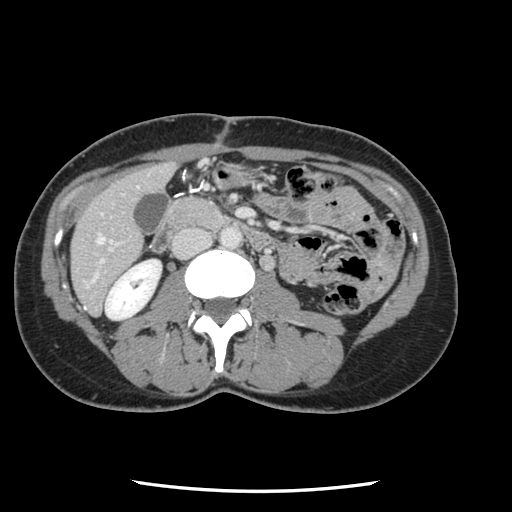
Contrast-enhanced abdominal CT, one axial slice; slice 28 of 134 in the series (ordered by position); intravenous contrast given; soft-tissue window (W 400 / L 40 HU); 512 × 512 image matrix, field of view 330 × 330 mm. Female patient, age 43 years. Case-level facts recorded for this patient, not image findings: diagnosis: colorectal cancer liver metastases, imaged before liver resection; multiple liver metastases: yes; largest metastasis: 3.4 cm; disease in both lobes: yes.
Outlined on this slice (manually delineated by an expert):
- hepatic veins: bounding box (x1, y1, x2, y2) in pixels: (96, 235, 103, 244)
- liver: (72, 165, 174, 314)
- planned liver remnant (the part of the liver to remain after resection): (72, 165, 173, 314)